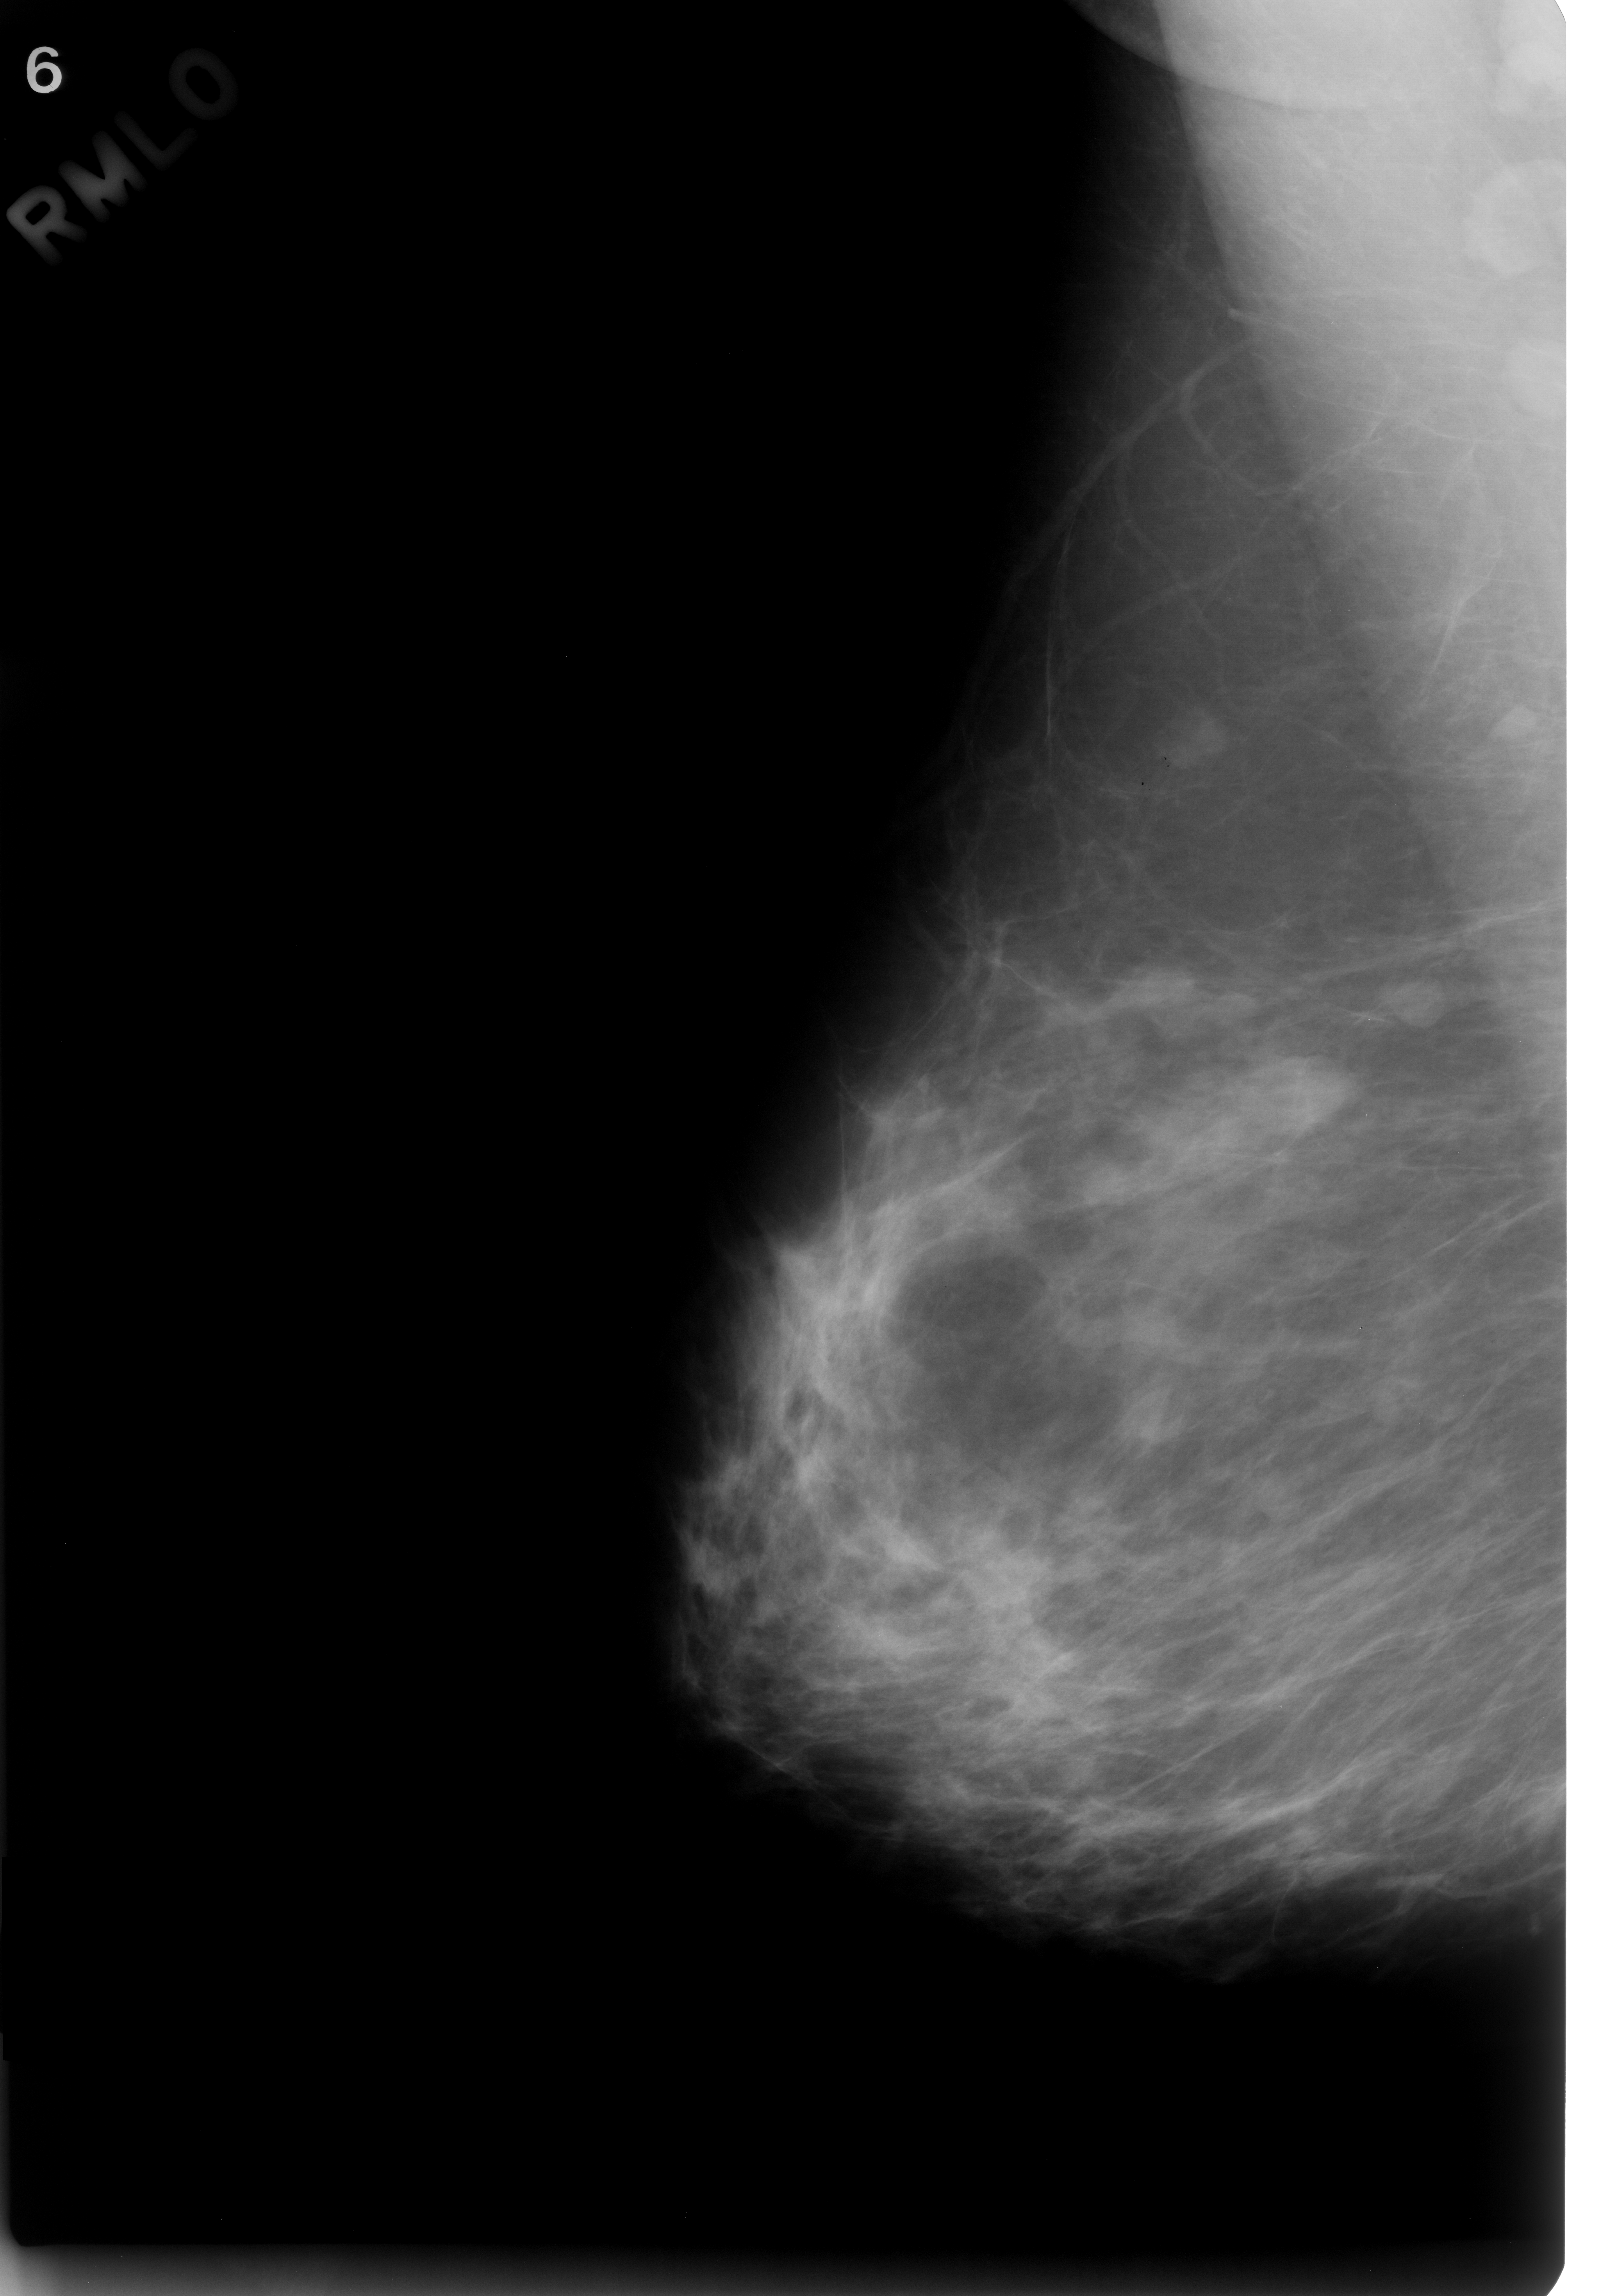
Mammogram (digitized film); right breast; mediolateral oblique (MLO) view; breast composition: scattered fibroglandular densities (BI-RADS density category 2 of 4); 1609 × 2296 image matrix.
Expert-marked regions of interest on this film, with their recorded descriptors:
- Finding 1 of 3: mass, shape lobulated, margins circumscribed; BI-RADS assessment category 3; pathology result (as recorded, not read from the image): benign: bounding box (x1, y1, x2, y2) in pixels: (1146, 691, 1238, 774)
- Finding 2 of 3: mass, shape lobulated, margins microlobulated; BI-RADS assessment category 3; subtlety rating 5 on a 1 (subtle) to 5 (obvious) scale; pathology result (as recorded, not read from the image): benign: (1216, 1036, 1353, 1142)
- Finding 3 of 3: mass, shape round, margins circumscribed; BI-RADS assessment category 3; subtlety rating 5 on a 1 (subtle) to 5 (obvious) scale; pathology (as recorded): benign: (1373, 950, 1470, 1033)